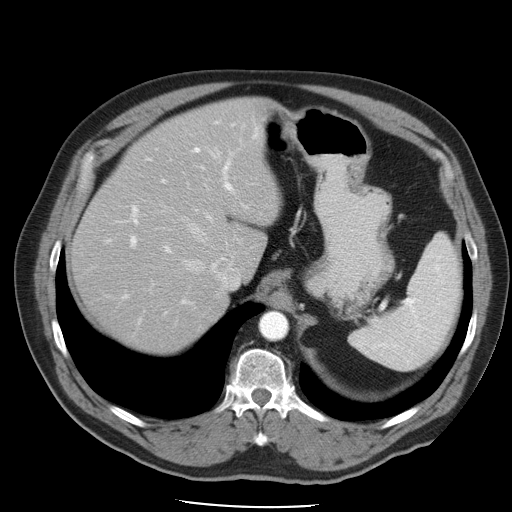
Contrast-enhanced abdominal CT, one axial slice. Position 36 of 49 along the scan axis. Reconstruction kernel STANDARD. 120 kVp. Intravenous contrast given. Soft-tissue window (W 400 / L 40 HU). 512 × 512 image matrix. Male patient, age 68 years. From the clinical record (not read from this slice): diagnosis: colorectal cancer liver metastases, imaged before liver resection; multiple liver metastases: yes; largest metastasis: 1.7 cm; disease in both lobes: no.
Structures marked on this image (expert manual segmentation):
- hepatic veins: bounding box [x1, y1, x2, y2] px = [161, 149, 240, 289]
- liver: [72, 100, 279, 353]
- planned liver remnant (the part of the liver to remain after resection): [72, 100, 279, 353]
- portal vein (with intrahepatic branches): [105, 121, 260, 323]